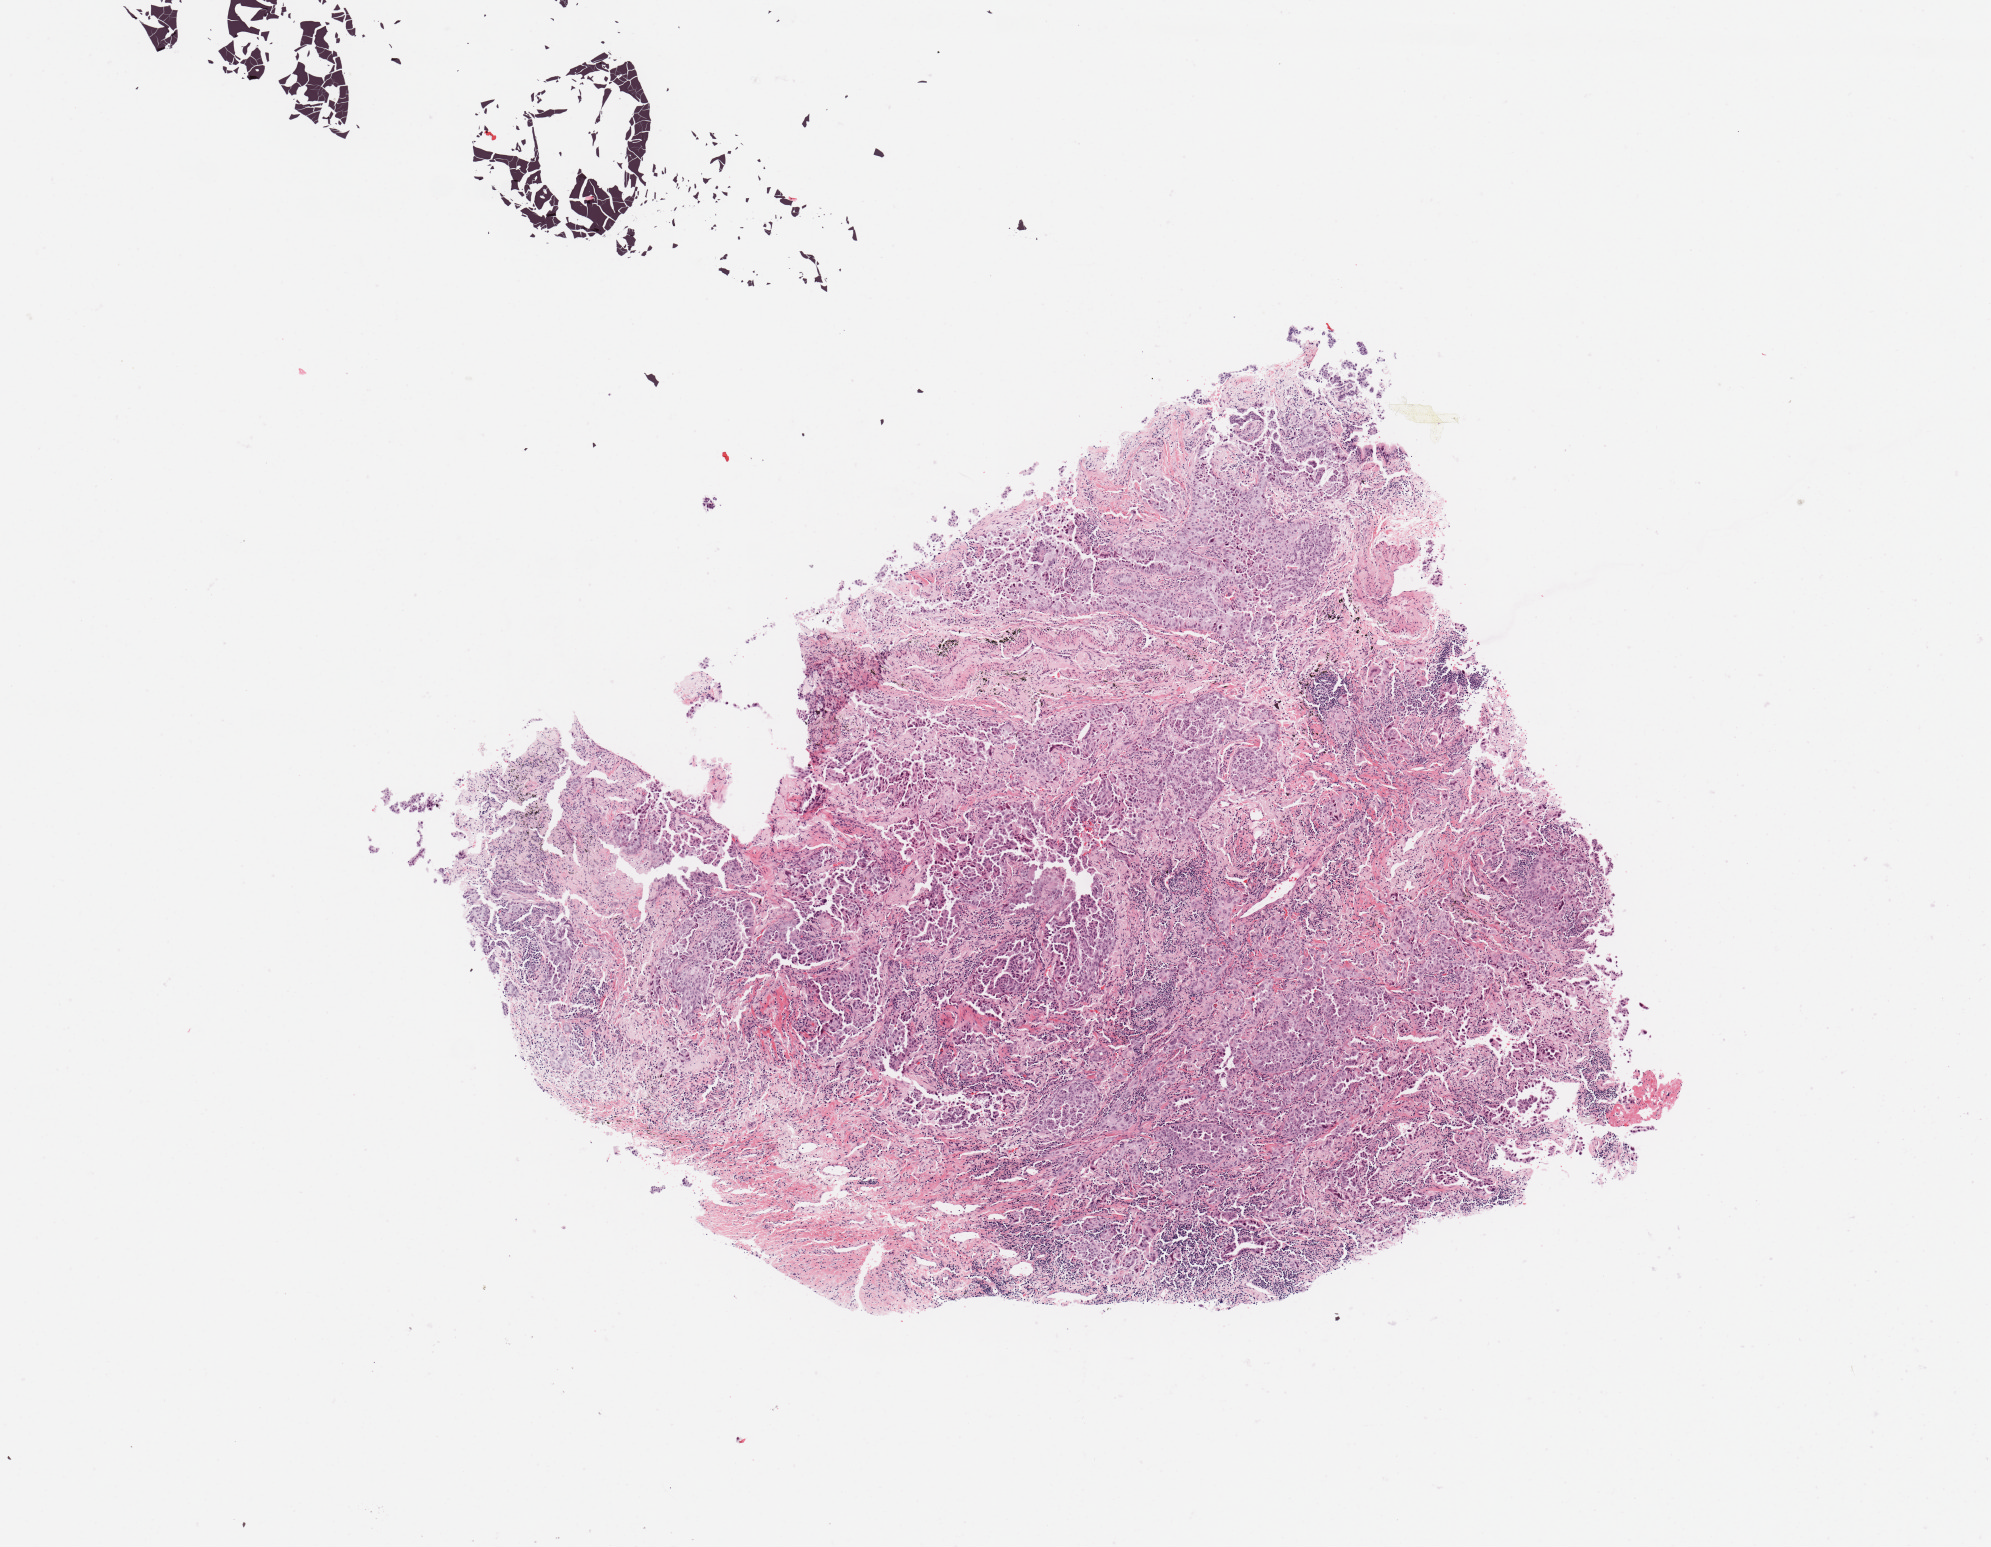
Whole-slide histology image, H&E-stained, low-resolution overview of the scanned area, about 7.9 x 6.1 mm (slide scanned at 20x). Tumour tissue sample, sampled site: lung. 50-year-old female patient.
Diagnosis: Adenocarcinoma, NOS.